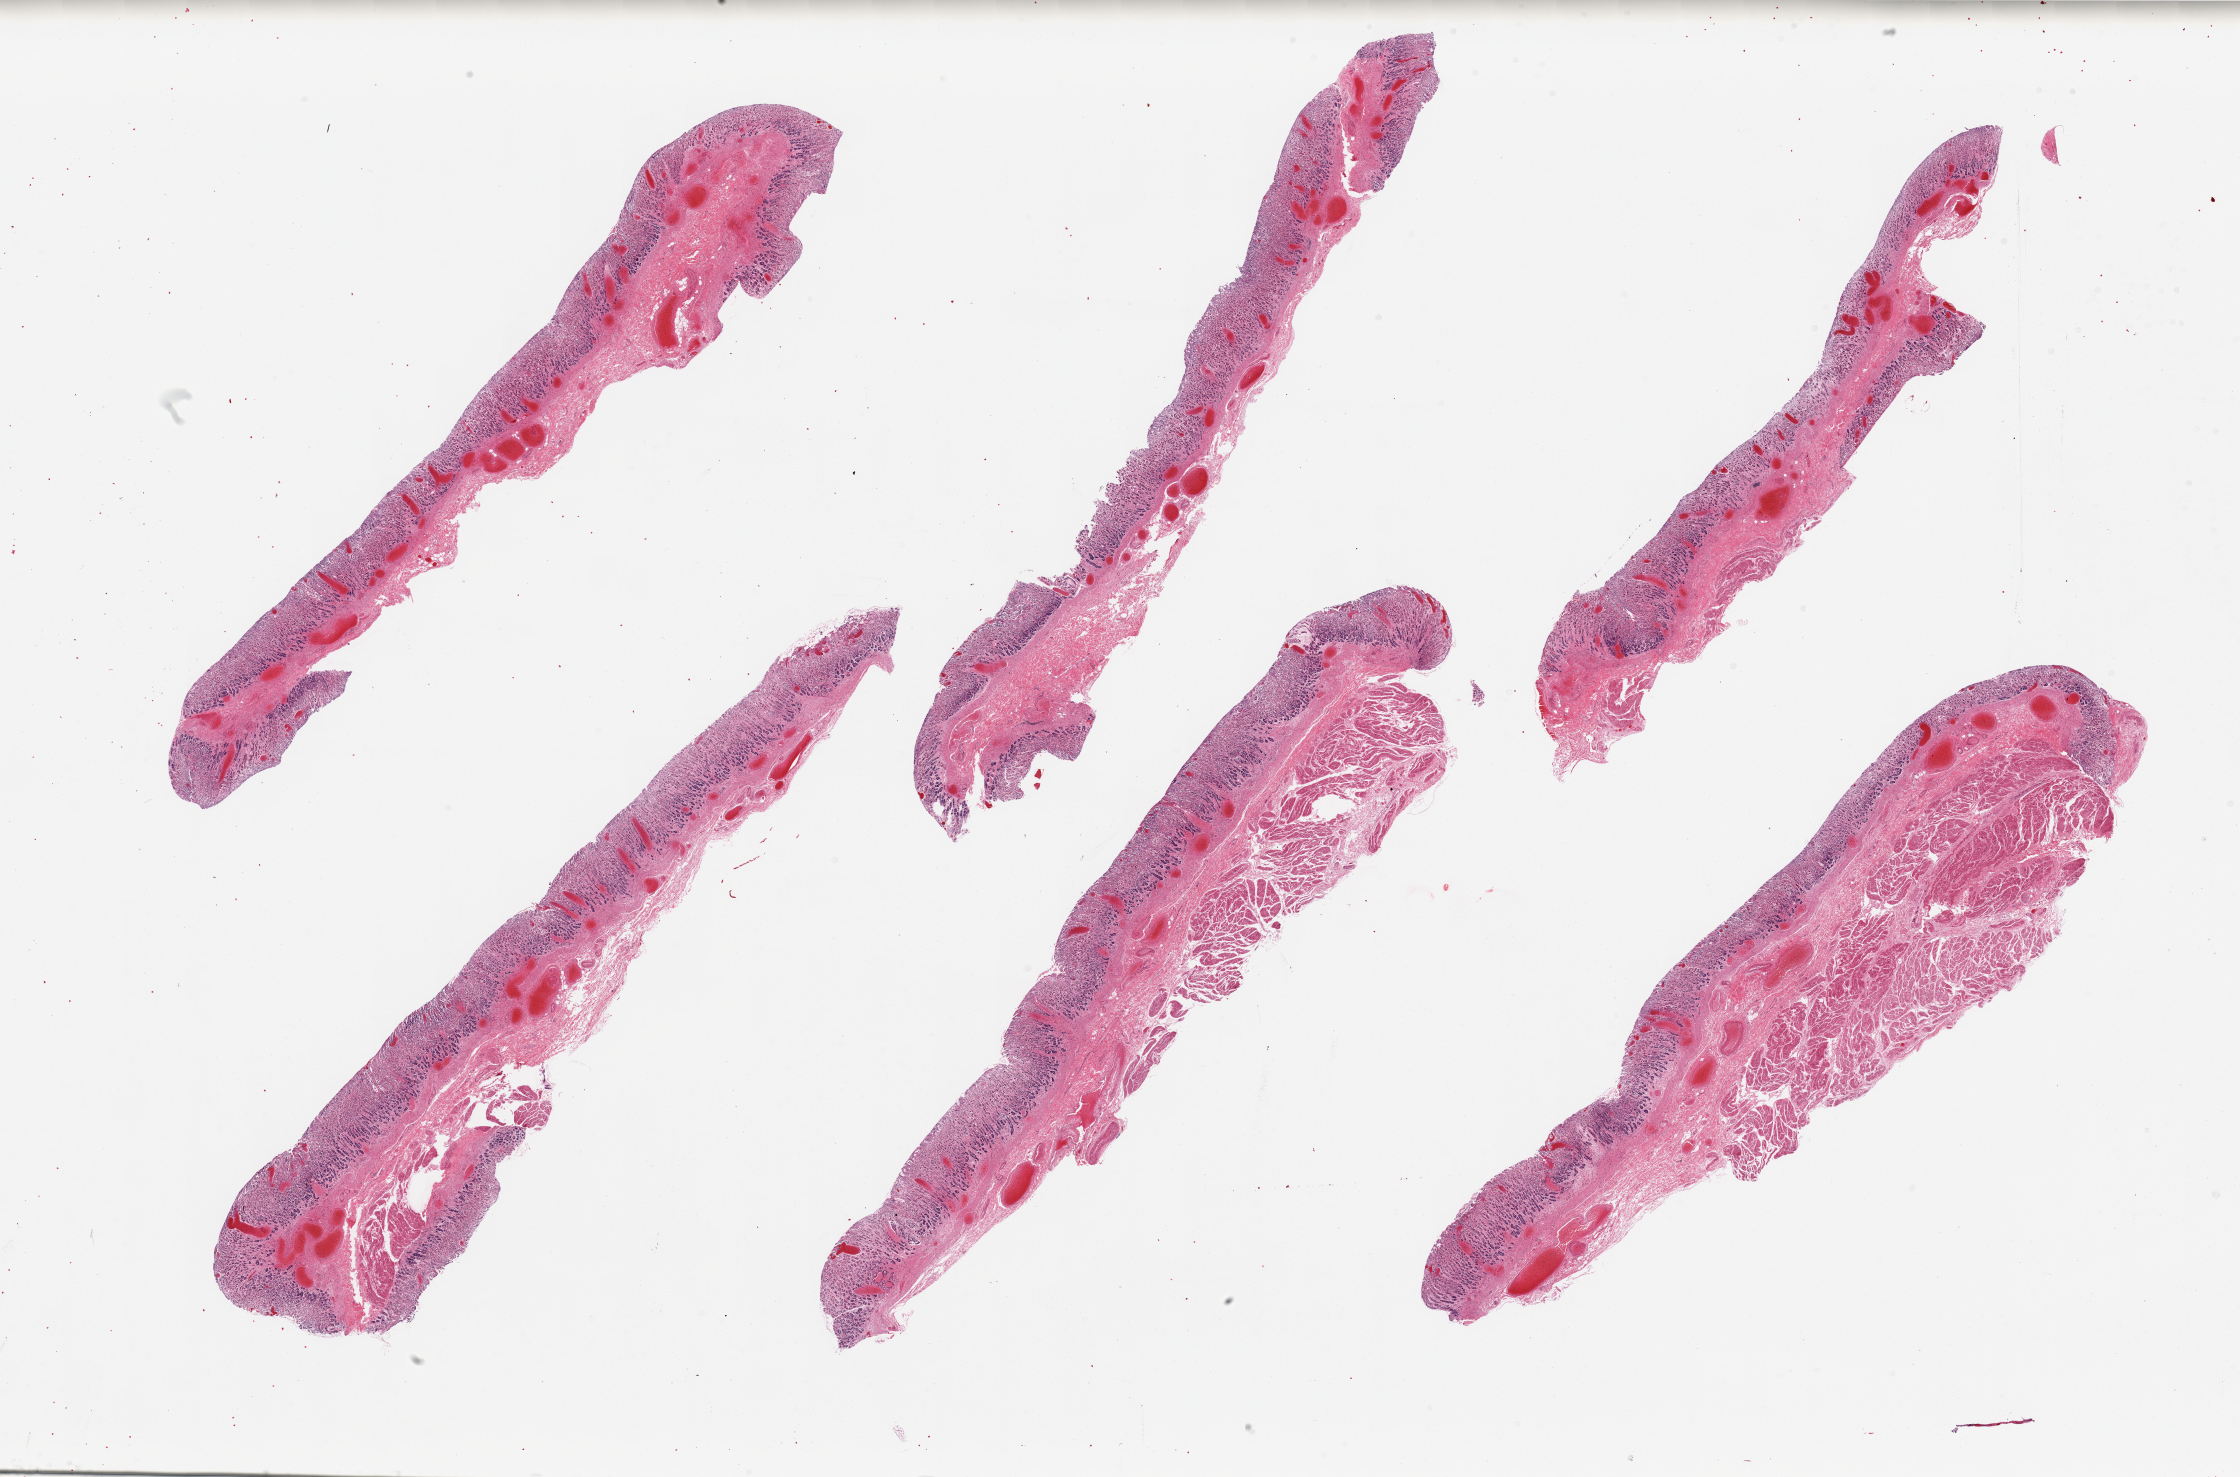
Digitized haematoxylin and eosin-stained section — a low-resolution overview of the entire scanned area, about 35.4 x 23.4 mm (from a 20x scan), PAXgene-fixed paraffin-embedded (PFPE) section, sampled site (target tissue): stomach, tissue donor sample. Donor sex: female.
Review note (as recorded): 6 pieces, mucosa is ~50-80% thickness, moderately autolyzed.